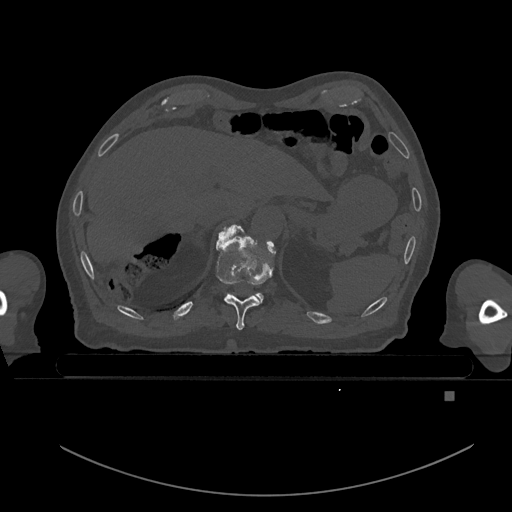
CT including the spine, one axial slice; slice 73 of 969 in the series (ordered by position); bone window (W 1800 / L 400 HU); 0.5 mm slice thickness; 512 × 512 image matrix, field of view 456 × 456 mm. Male patient, age 82 years. Case-level facts recorded for this patient, not image findings: primary cancer: prostate; vertebrae with lytic lesions (as recorded): T11, T9, T8, T2.
Outlined on this slice (semi-automatically segmented with operator editing):
- T10 vertebra: bounding box <216,225,274,331> (left, top, right, bottom; pixels)
- T11 vertebra: <222,227,272,303>